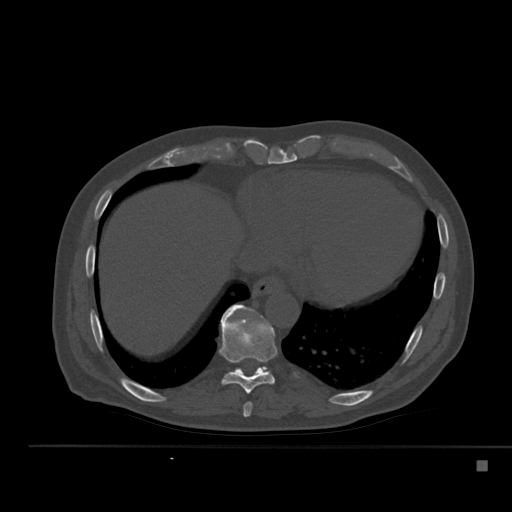
CT including the spine, one axial slice; position 286 of 517 along the scan axis; bone window (W 1800 / L 400 HU); 1.5 mm slice thickness; 512 × 512 image matrix, field of view 408 × 408 mm. Patient: male, 70 years. From the clinical record (not read from this slice): primary cancer: renal.
Annotated regions visible in this slice (semi-automatically segmented with operator editing):
- T10 vertebra: bounding box (x1, y1, x2, y2) in pixels: (224, 304, 267, 376)
- T8 vertebra: (243, 402, 253, 417)
- T9 vertebra: (219, 305, 277, 394)